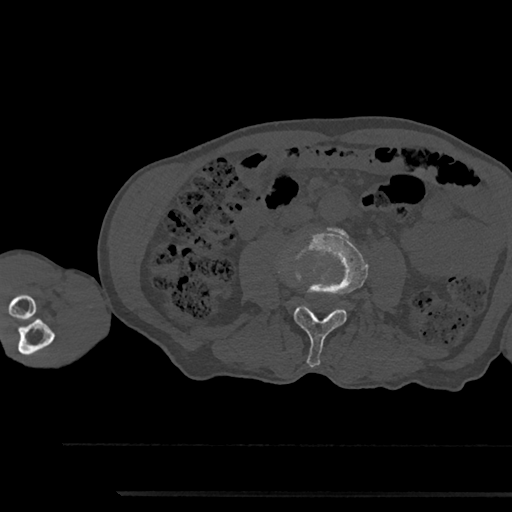
CT including the spine, one axial slice; slice 465 of 797 in the series (ordered by position); bone window (W 1800 / L 400 HU); 0.5 mm slice thickness; 512 × 512 image matrix, field of view 367 × 367 mm. Male patient, age 79 years. From the clinical record (not read from this slice): primary cancer: prostate.
Outlined on this slice (semi-automatic segmentation, software-assisted and operator-edited):
- L3 vertebra: box from (x=282, y=228) to (x=368, y=367) px